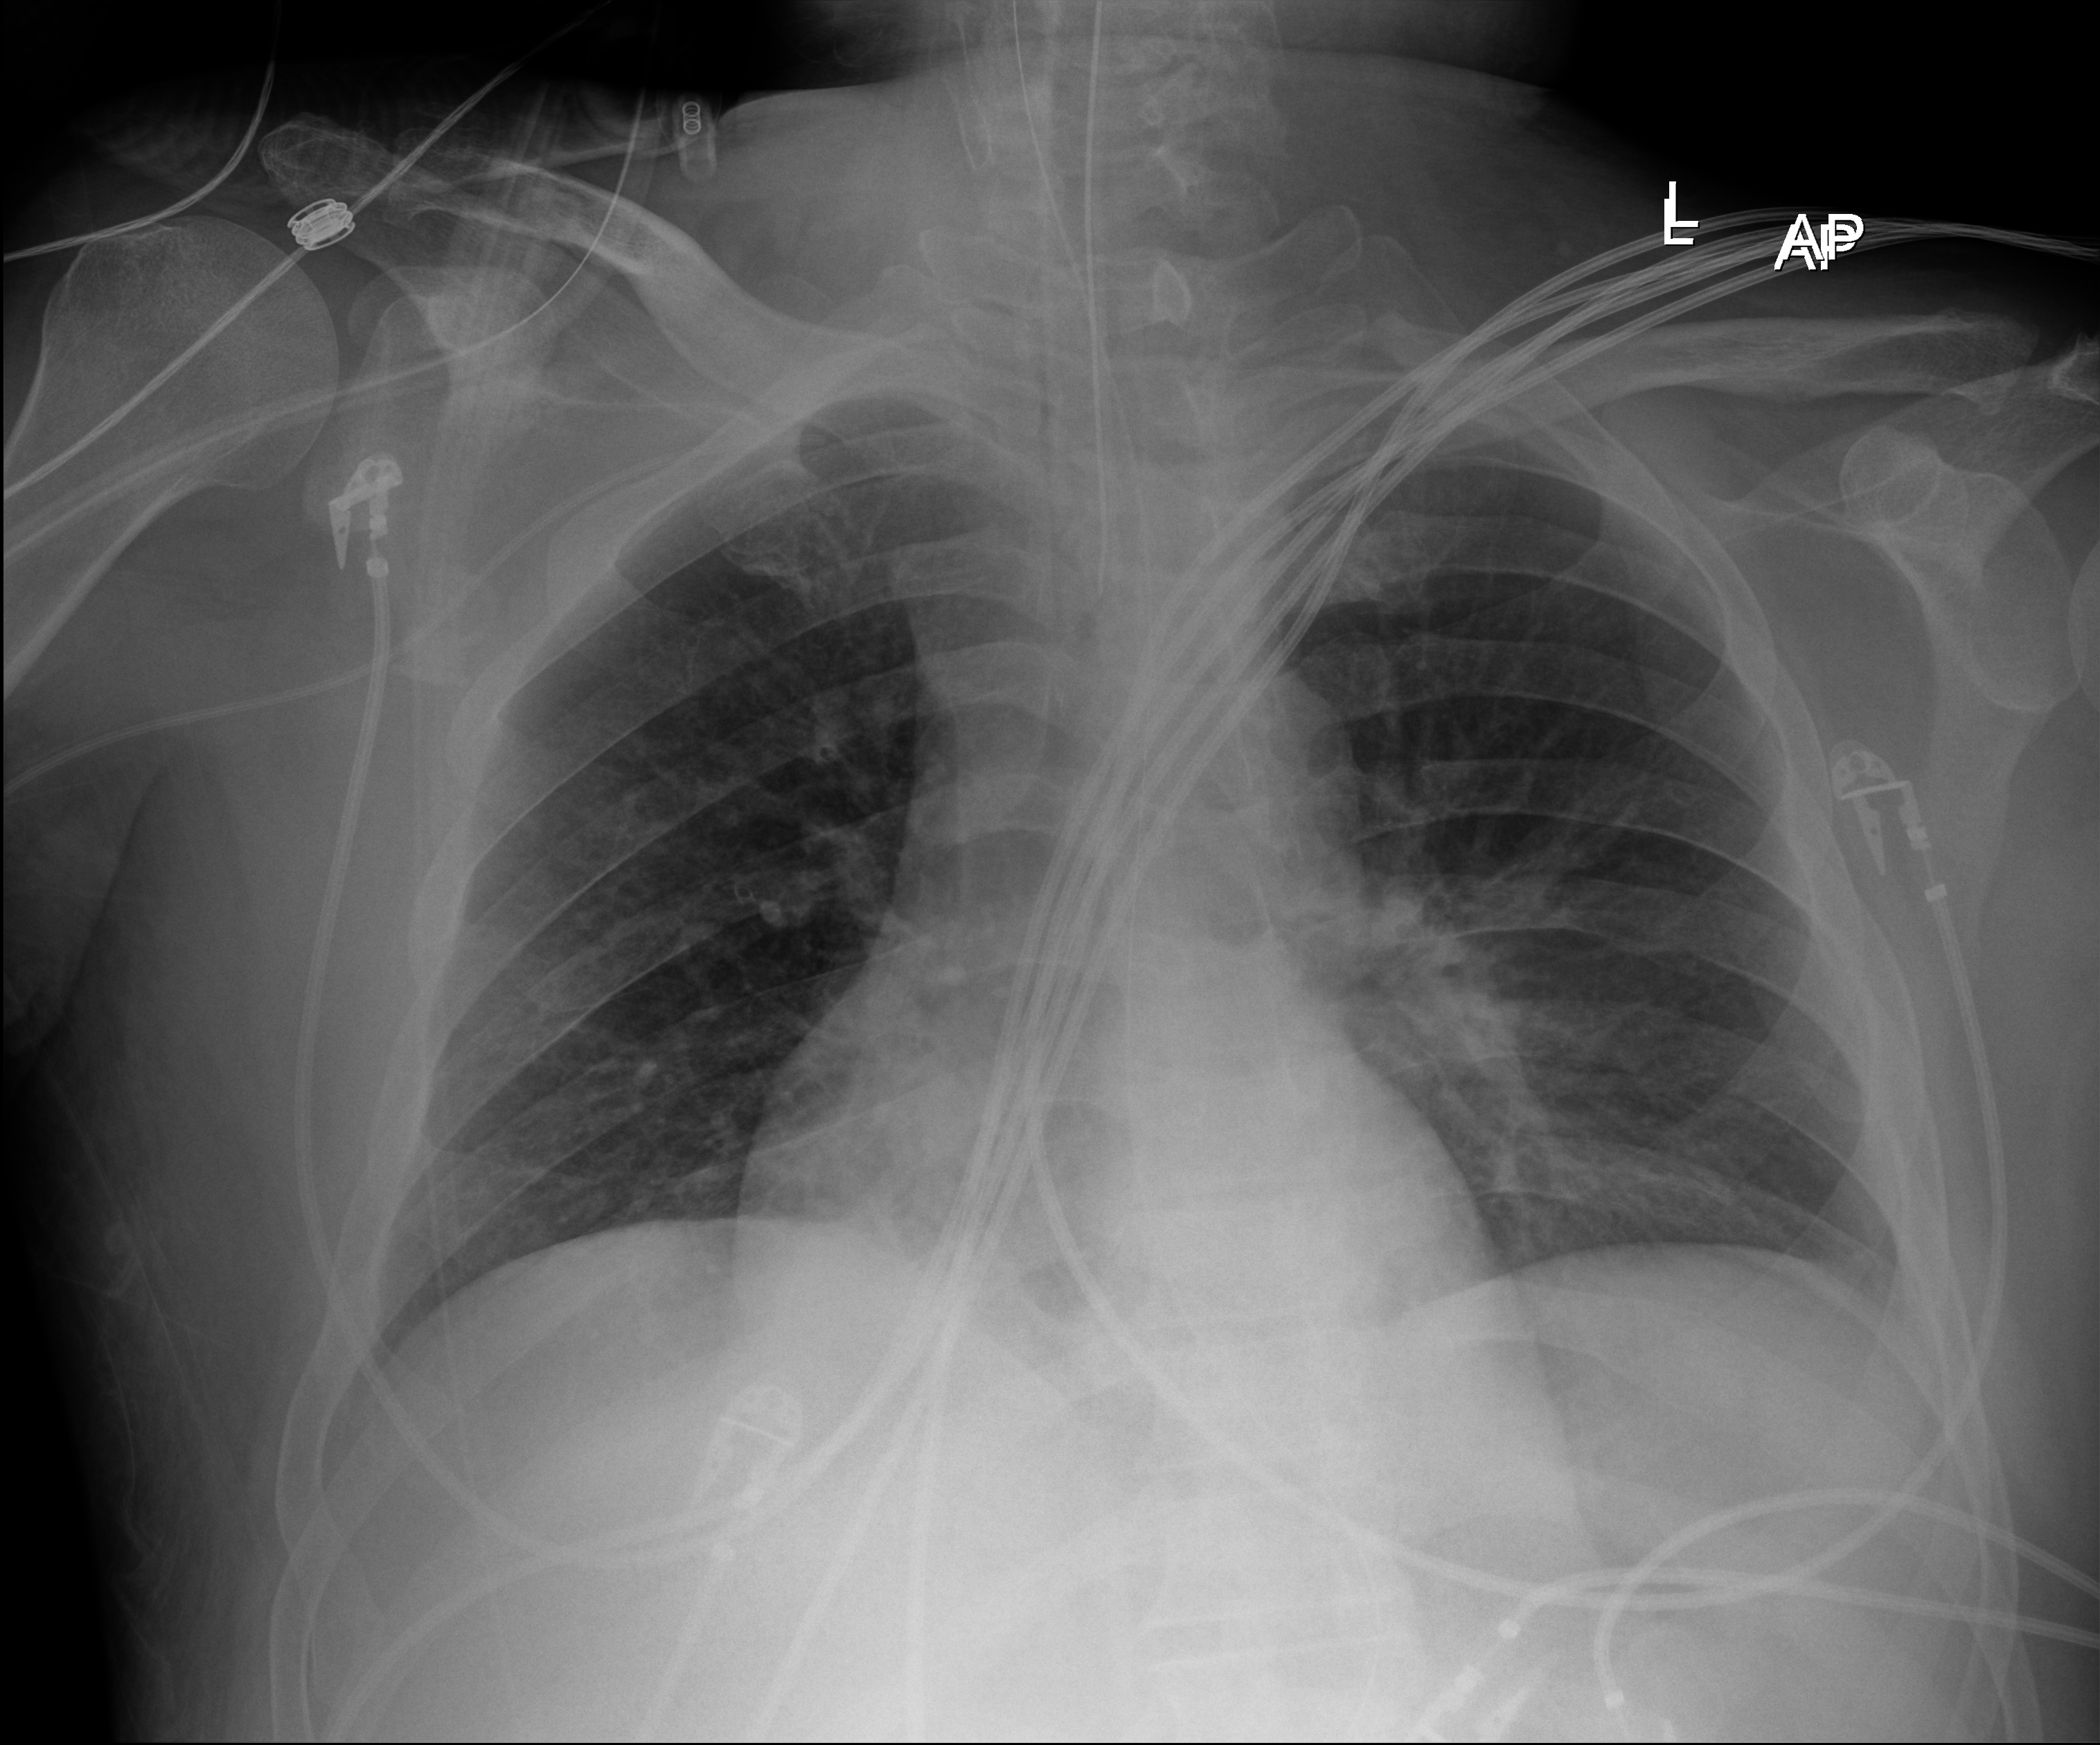
Chest X-ray (portable); anteroposterior (AP) projection. Patient hospitalised with COVID-19; male, aged 18–59 years.
Hospital-stay facts (about this admission, not read from this image; timing relative to this image not recorded):
- mechanically ventilated during this hospital stay: yes
- admitted to intensive care during this hospital stay: yes